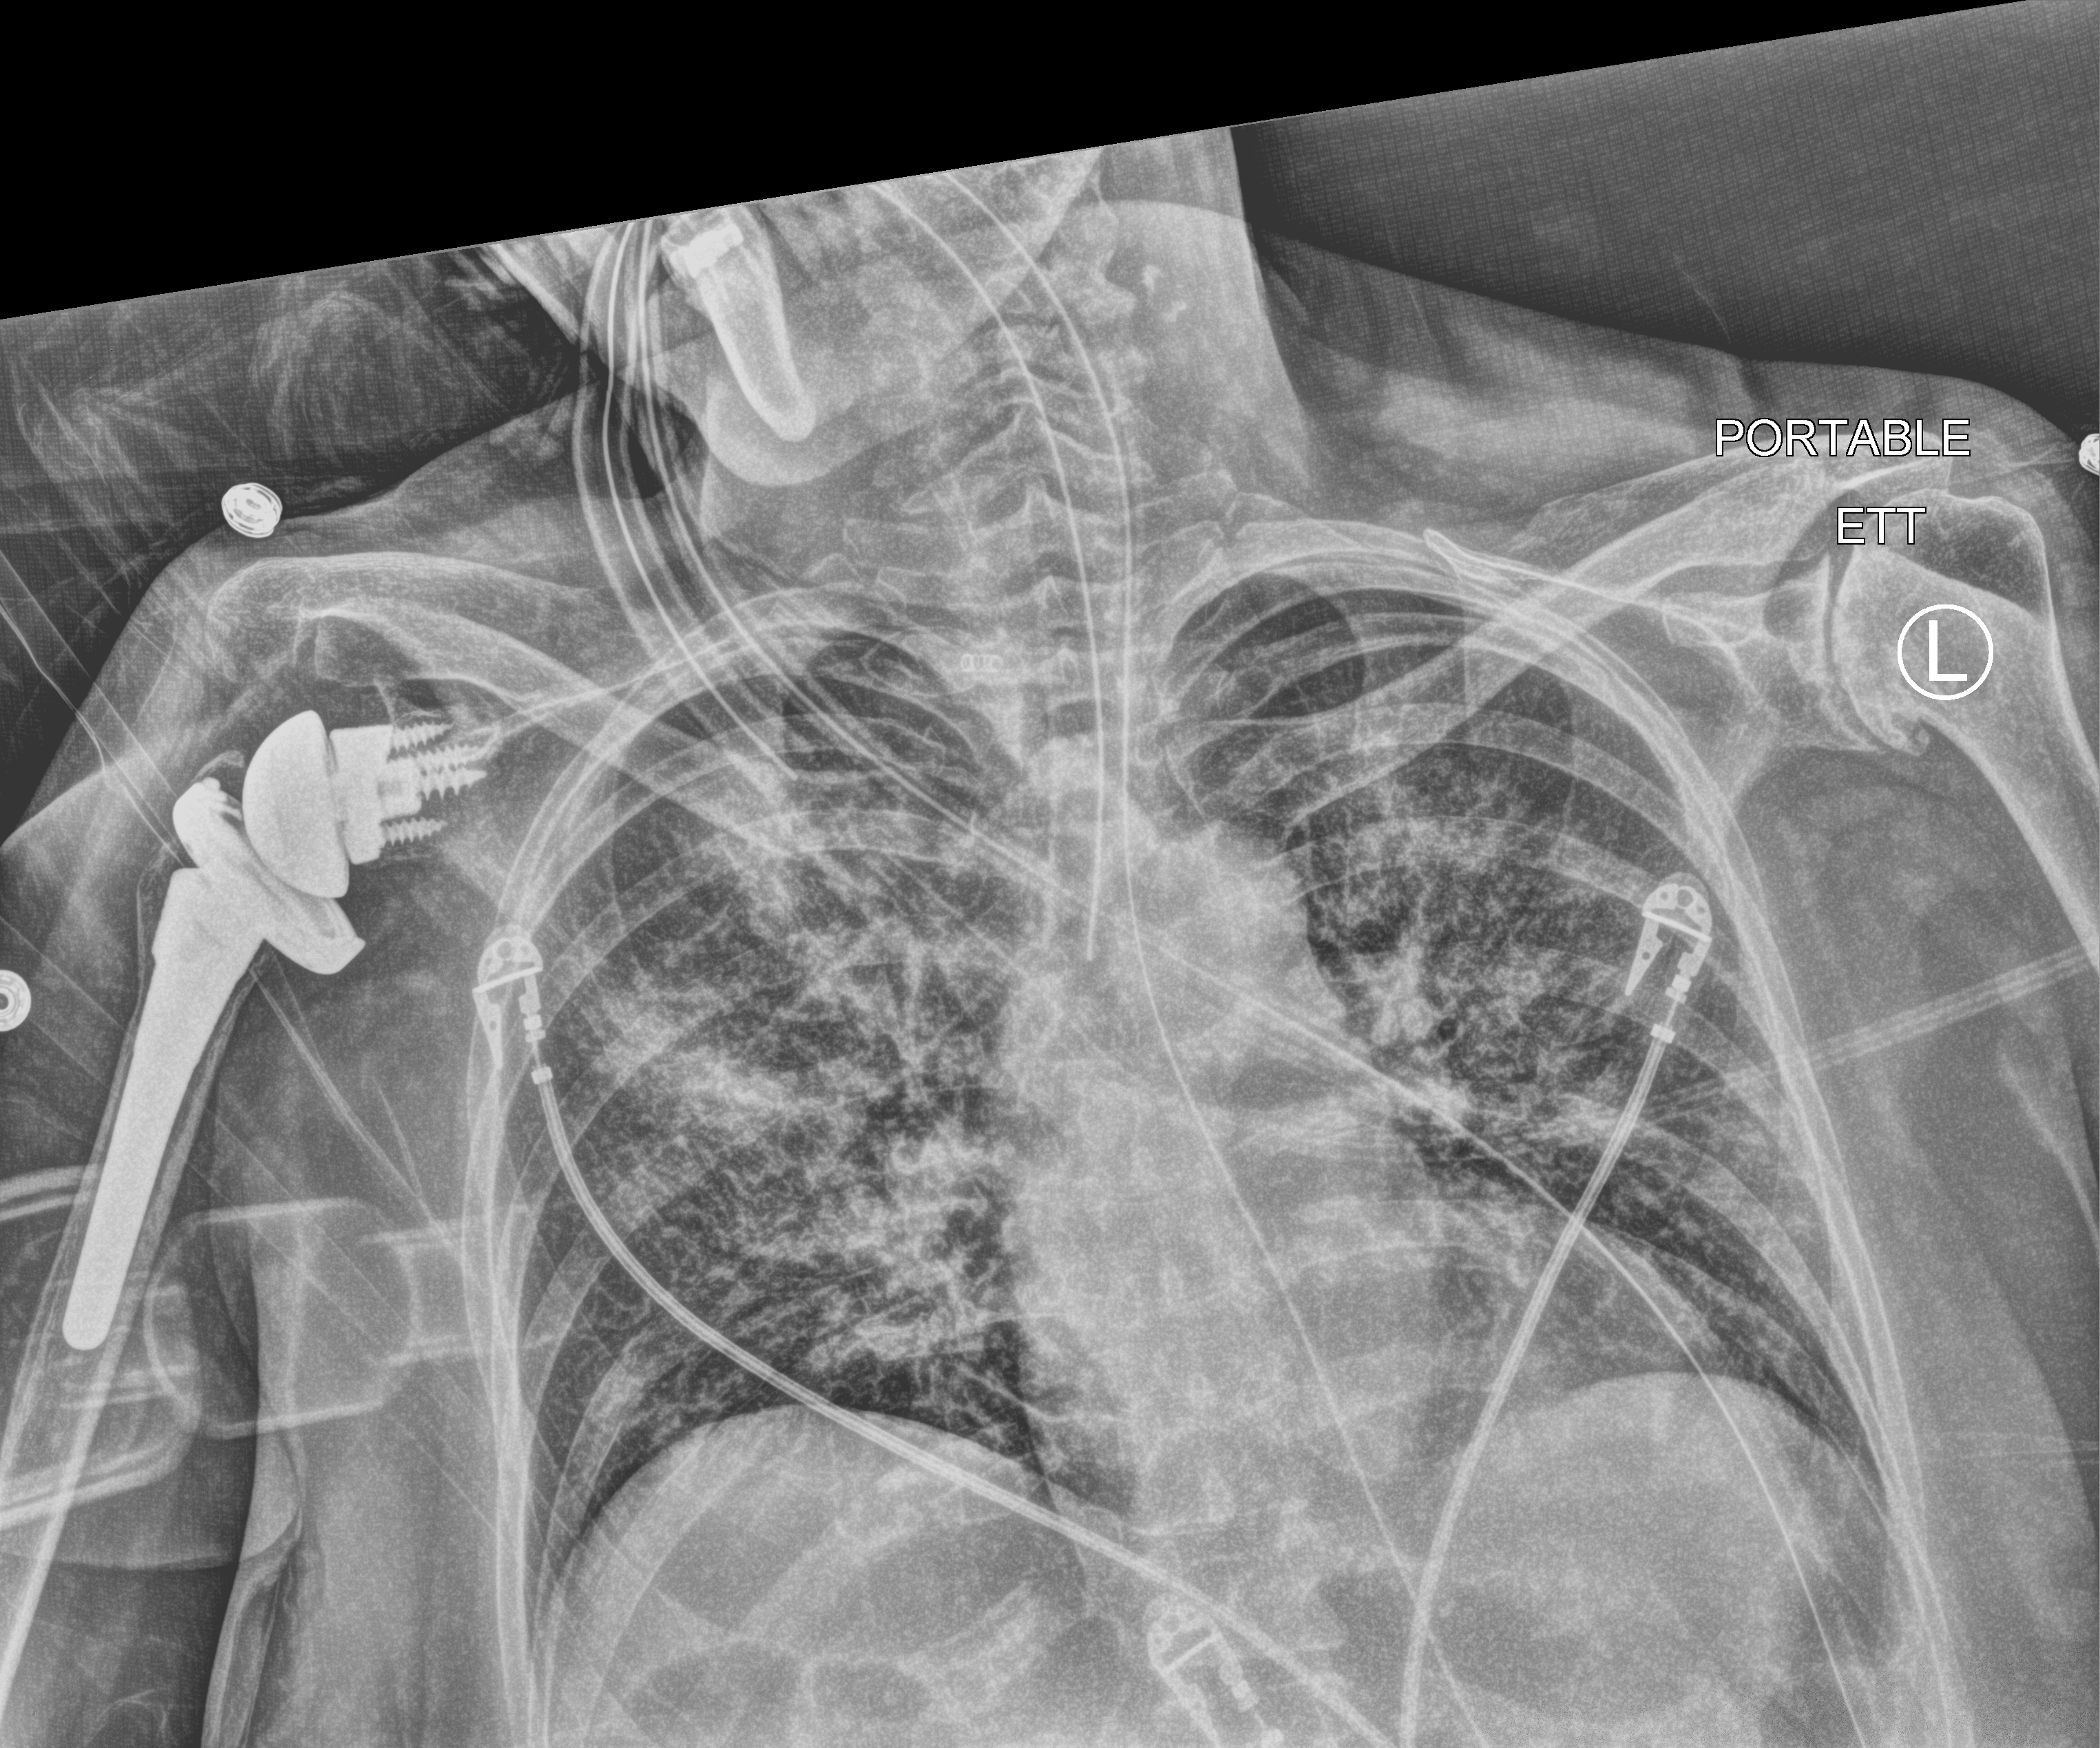
Chest X-ray (portable), anteroposterior (AP) projection. Female patient hospitalised with COVID-19, age 60–74 years.
Admission-level facts for this patient (not findings on this image; timing relative to this image not recorded):
- mechanically ventilated during this hospital stay: yes